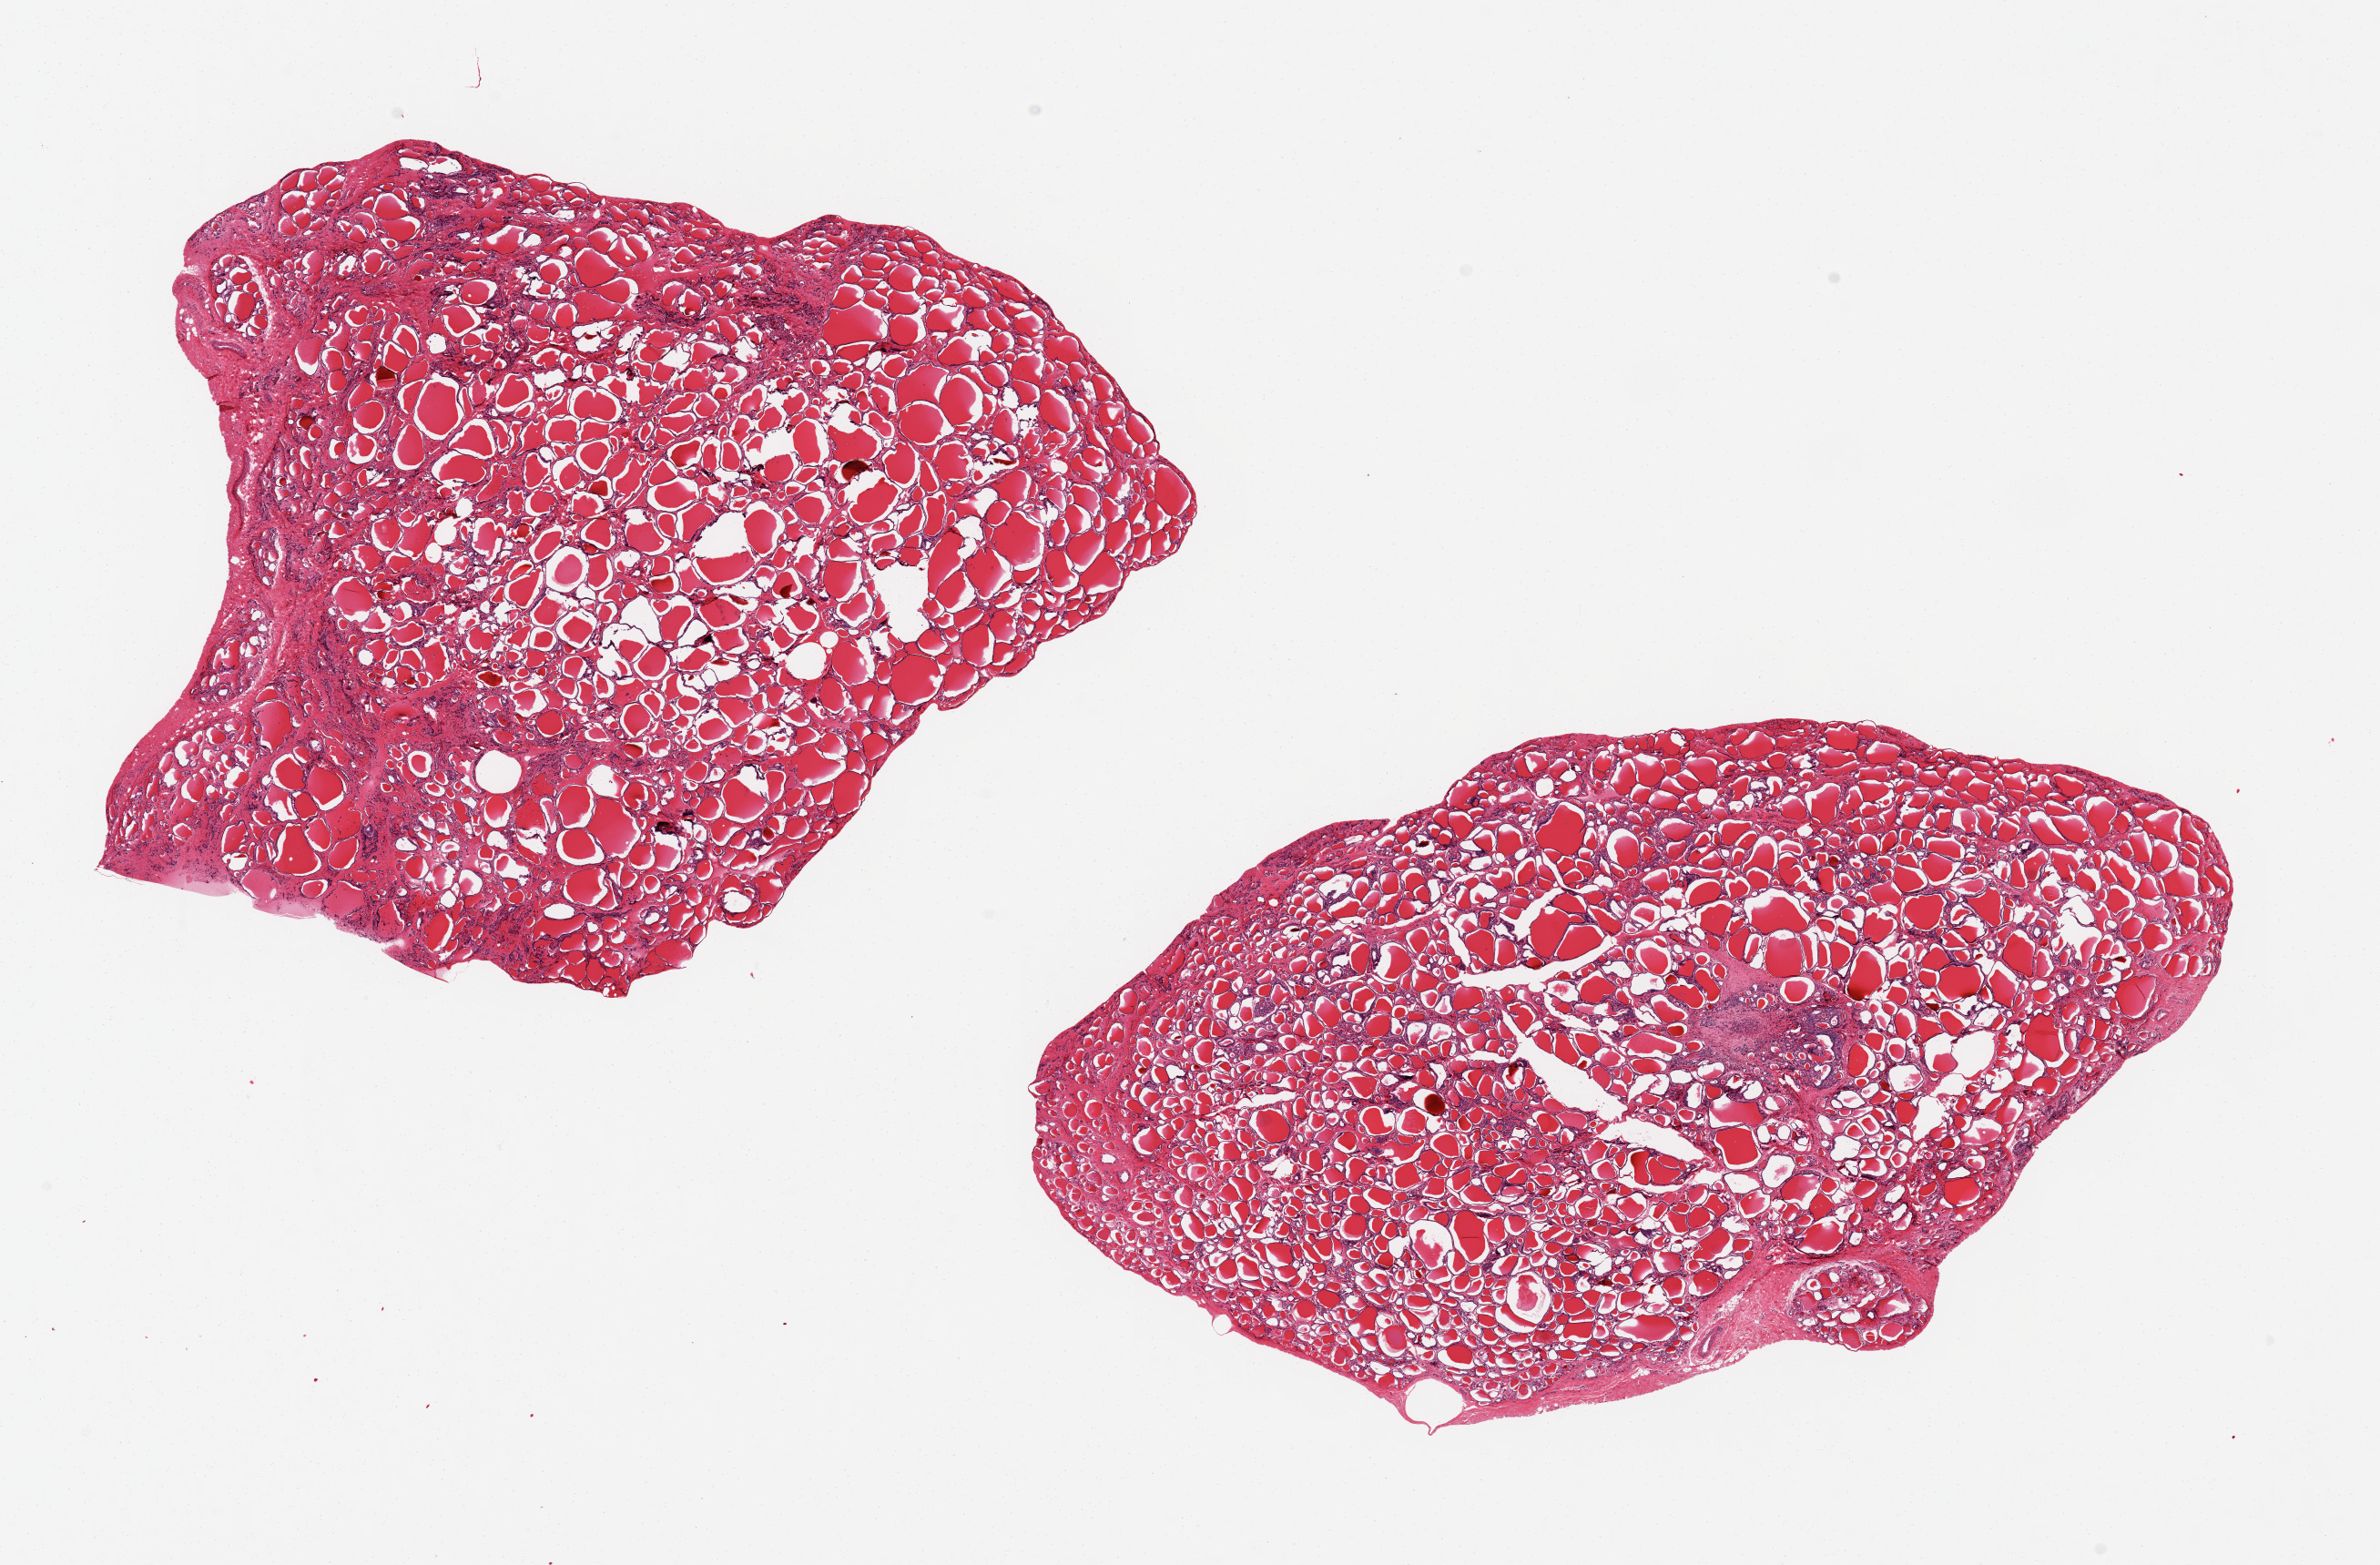
Haematoxylin and eosin whole-slide image — whole scanned area (about 20.7 x 13.6 mm) shown as a low-resolution overview, PAXgene-fixed paraffin-embedded (PFPE) section, sampled site (target tissue): thyroid, tissue donor sample. Female donor.
Reviewer comment on this tissue sample: 2 pieces, 11x5 & 9x7 mm.